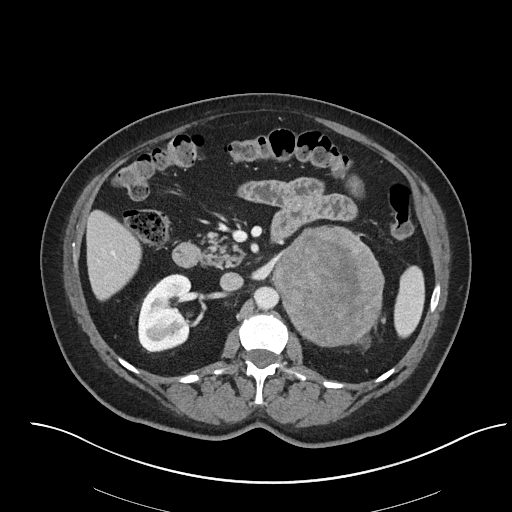
Contrast-enhanced abdominal CT, one axial slice; slice 38 of 92 in the series (ordered by position); reconstruction kernel I40f/2; 120 kVp; soft-tissue window (W 400 / L 40 HU); 3 mm slice thickness; 512 × 512 image matrix, field of view 440 × 440 mm. Female patient, age 53 years. Case-level facts recorded for this patient, not image findings: diagnosis: adrenocortical carcinoma; tumour side: left adrenal; tumour size at pathology: 9 cm.
Structures marked on this image (semi-automatically segmented with operator editing):
- mass: box from (x=274, y=227) to (x=383, y=344) px